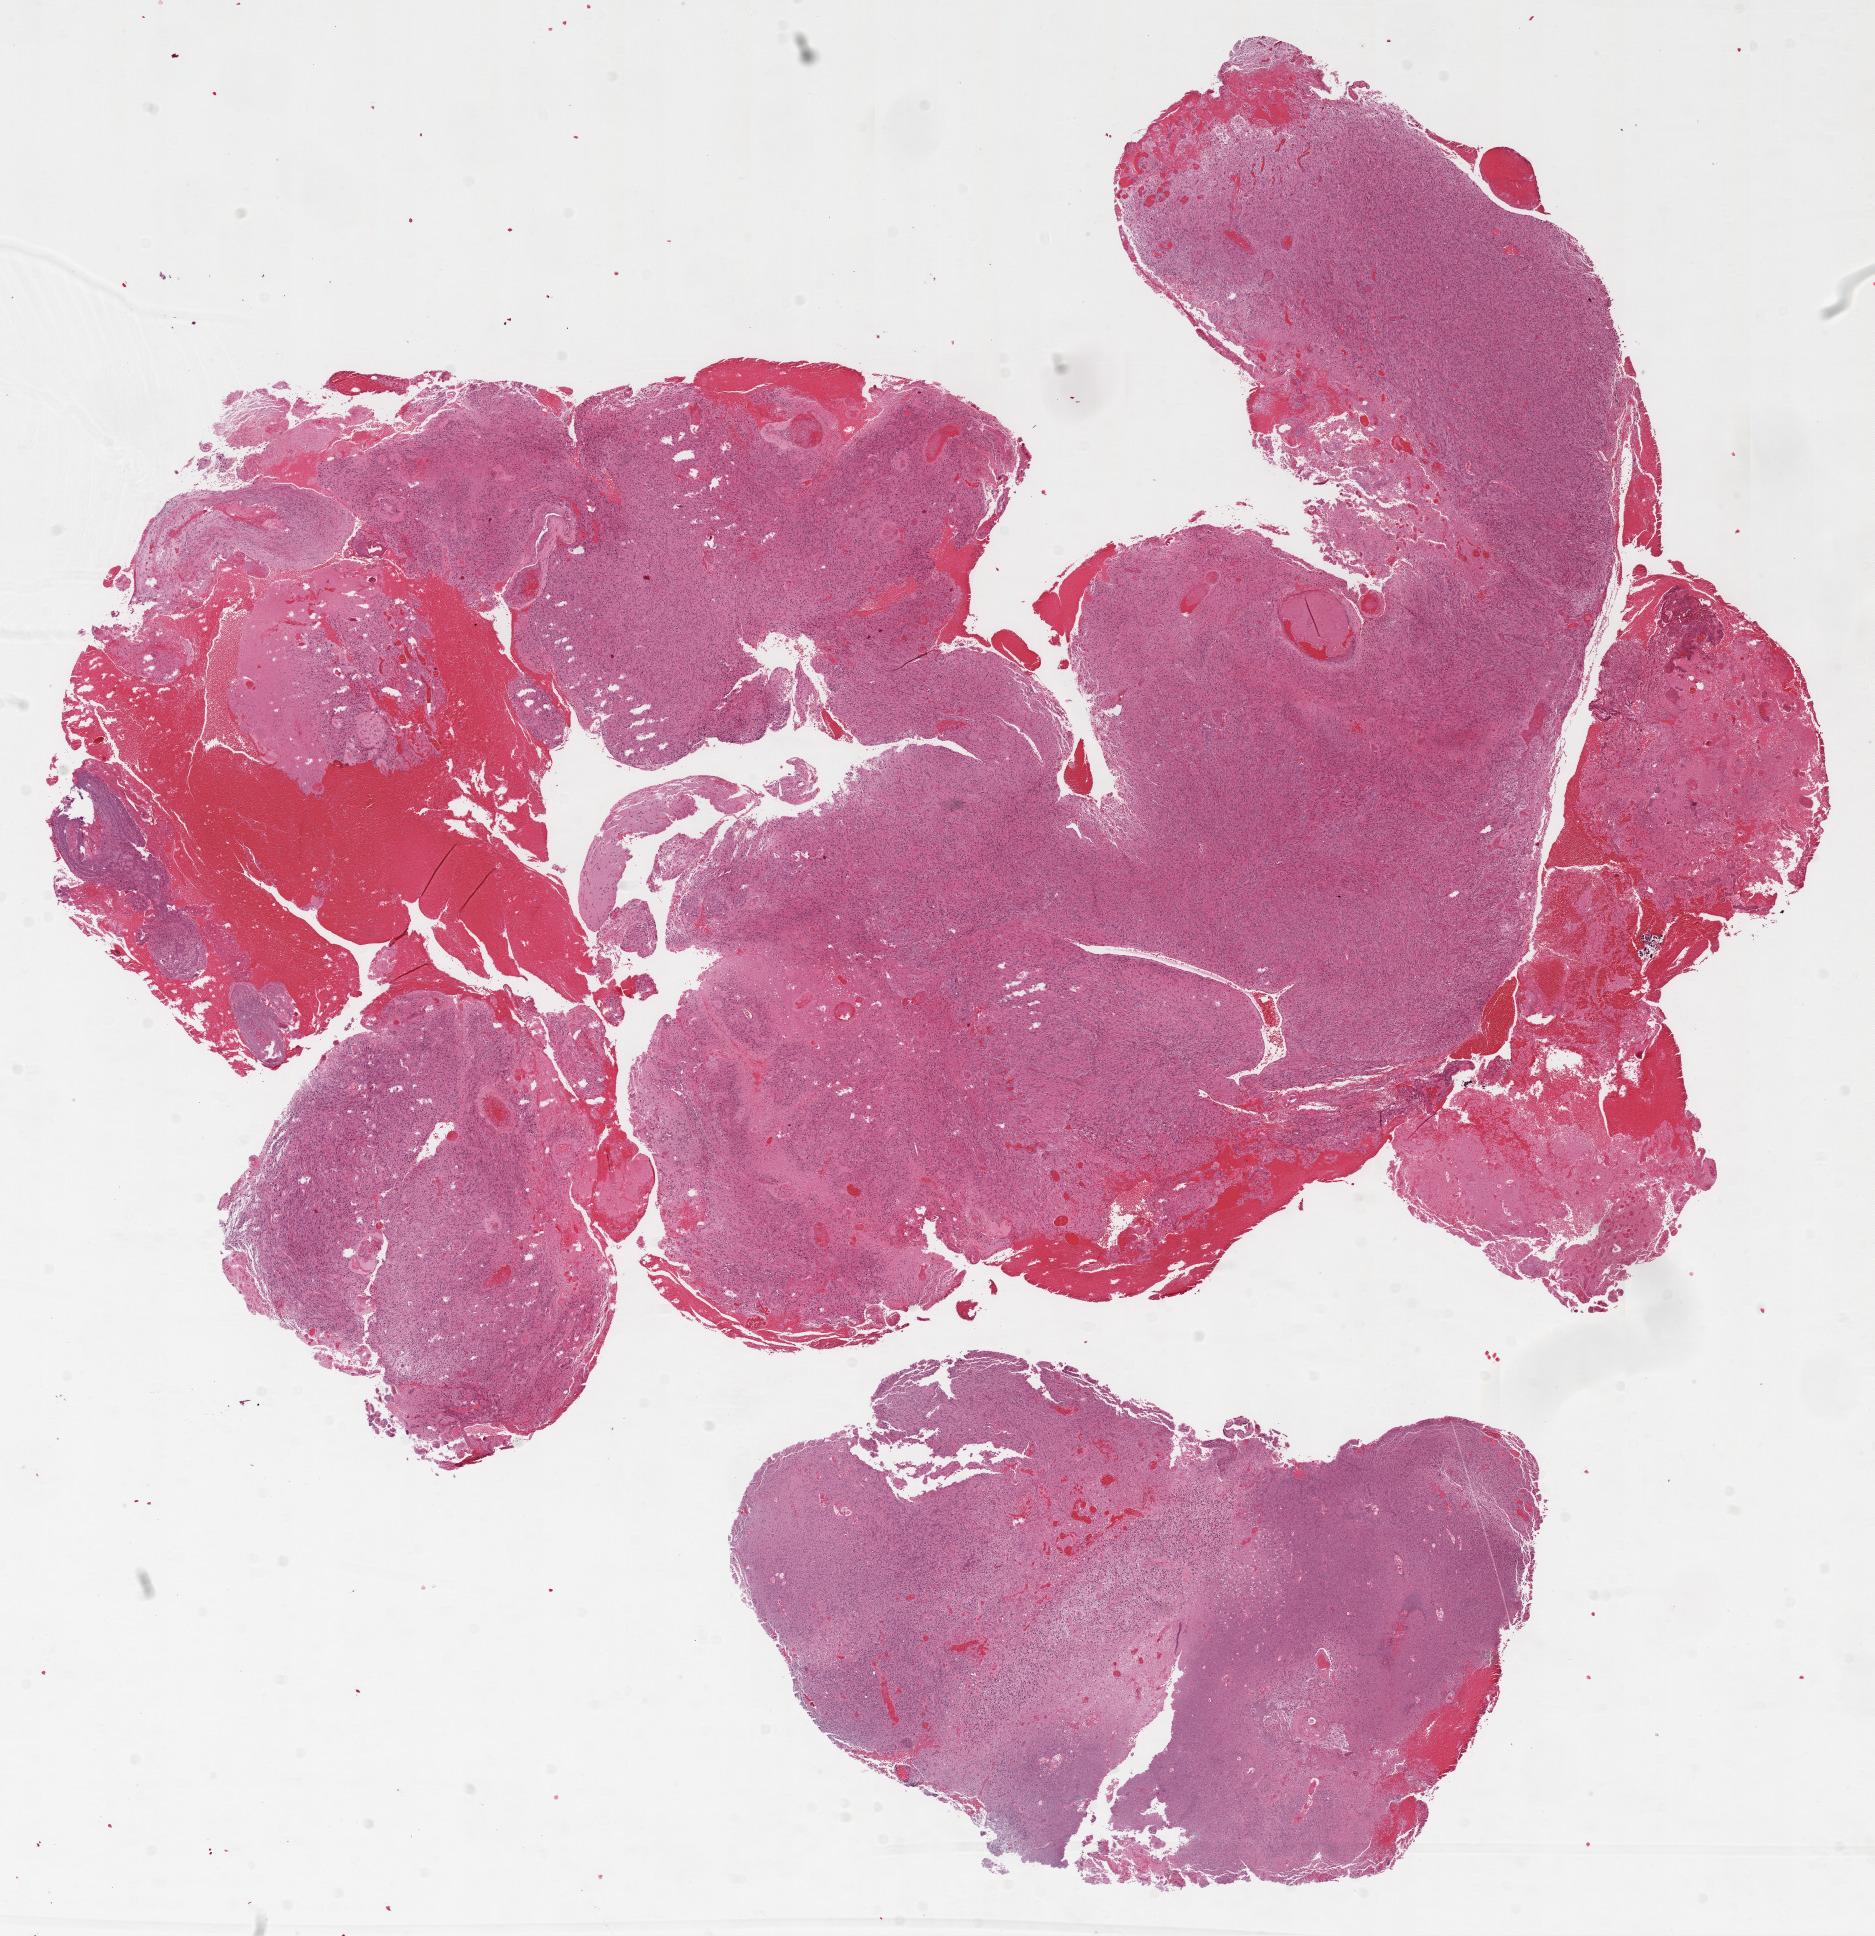
H&E whole-slide image, whole scanned area (about 15.0 x 15.5 mm, slide scanned at 20x) shown as a low-resolution overview; FFPE section; sample: primary tumour, brain. Female patient; age at initial diagnosis 58 years.
Pathologic diagnosis: Glioblastoma.